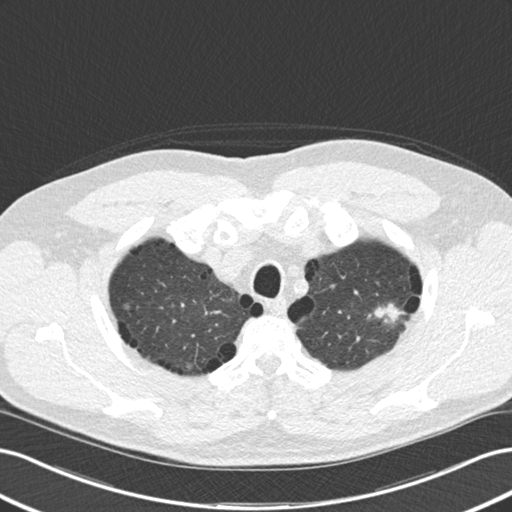
Low-dose screening chest CT, one axial slice. Slice 142 of 177 in the series (ordered by position). Reconstruction kernel B30f. Lung window (W 1500 / L -600 HU). 2 mm slice thickness. 512 × 512 image matrix, field of view 360 × 360 mm.
Annotated regions visible in this slice (expert manual segmentation):
- lesion 1 (tumor, upper lobe of left lung): bounding box (x1, y1, x2, y2) in pixels: (374, 303, 405, 324)